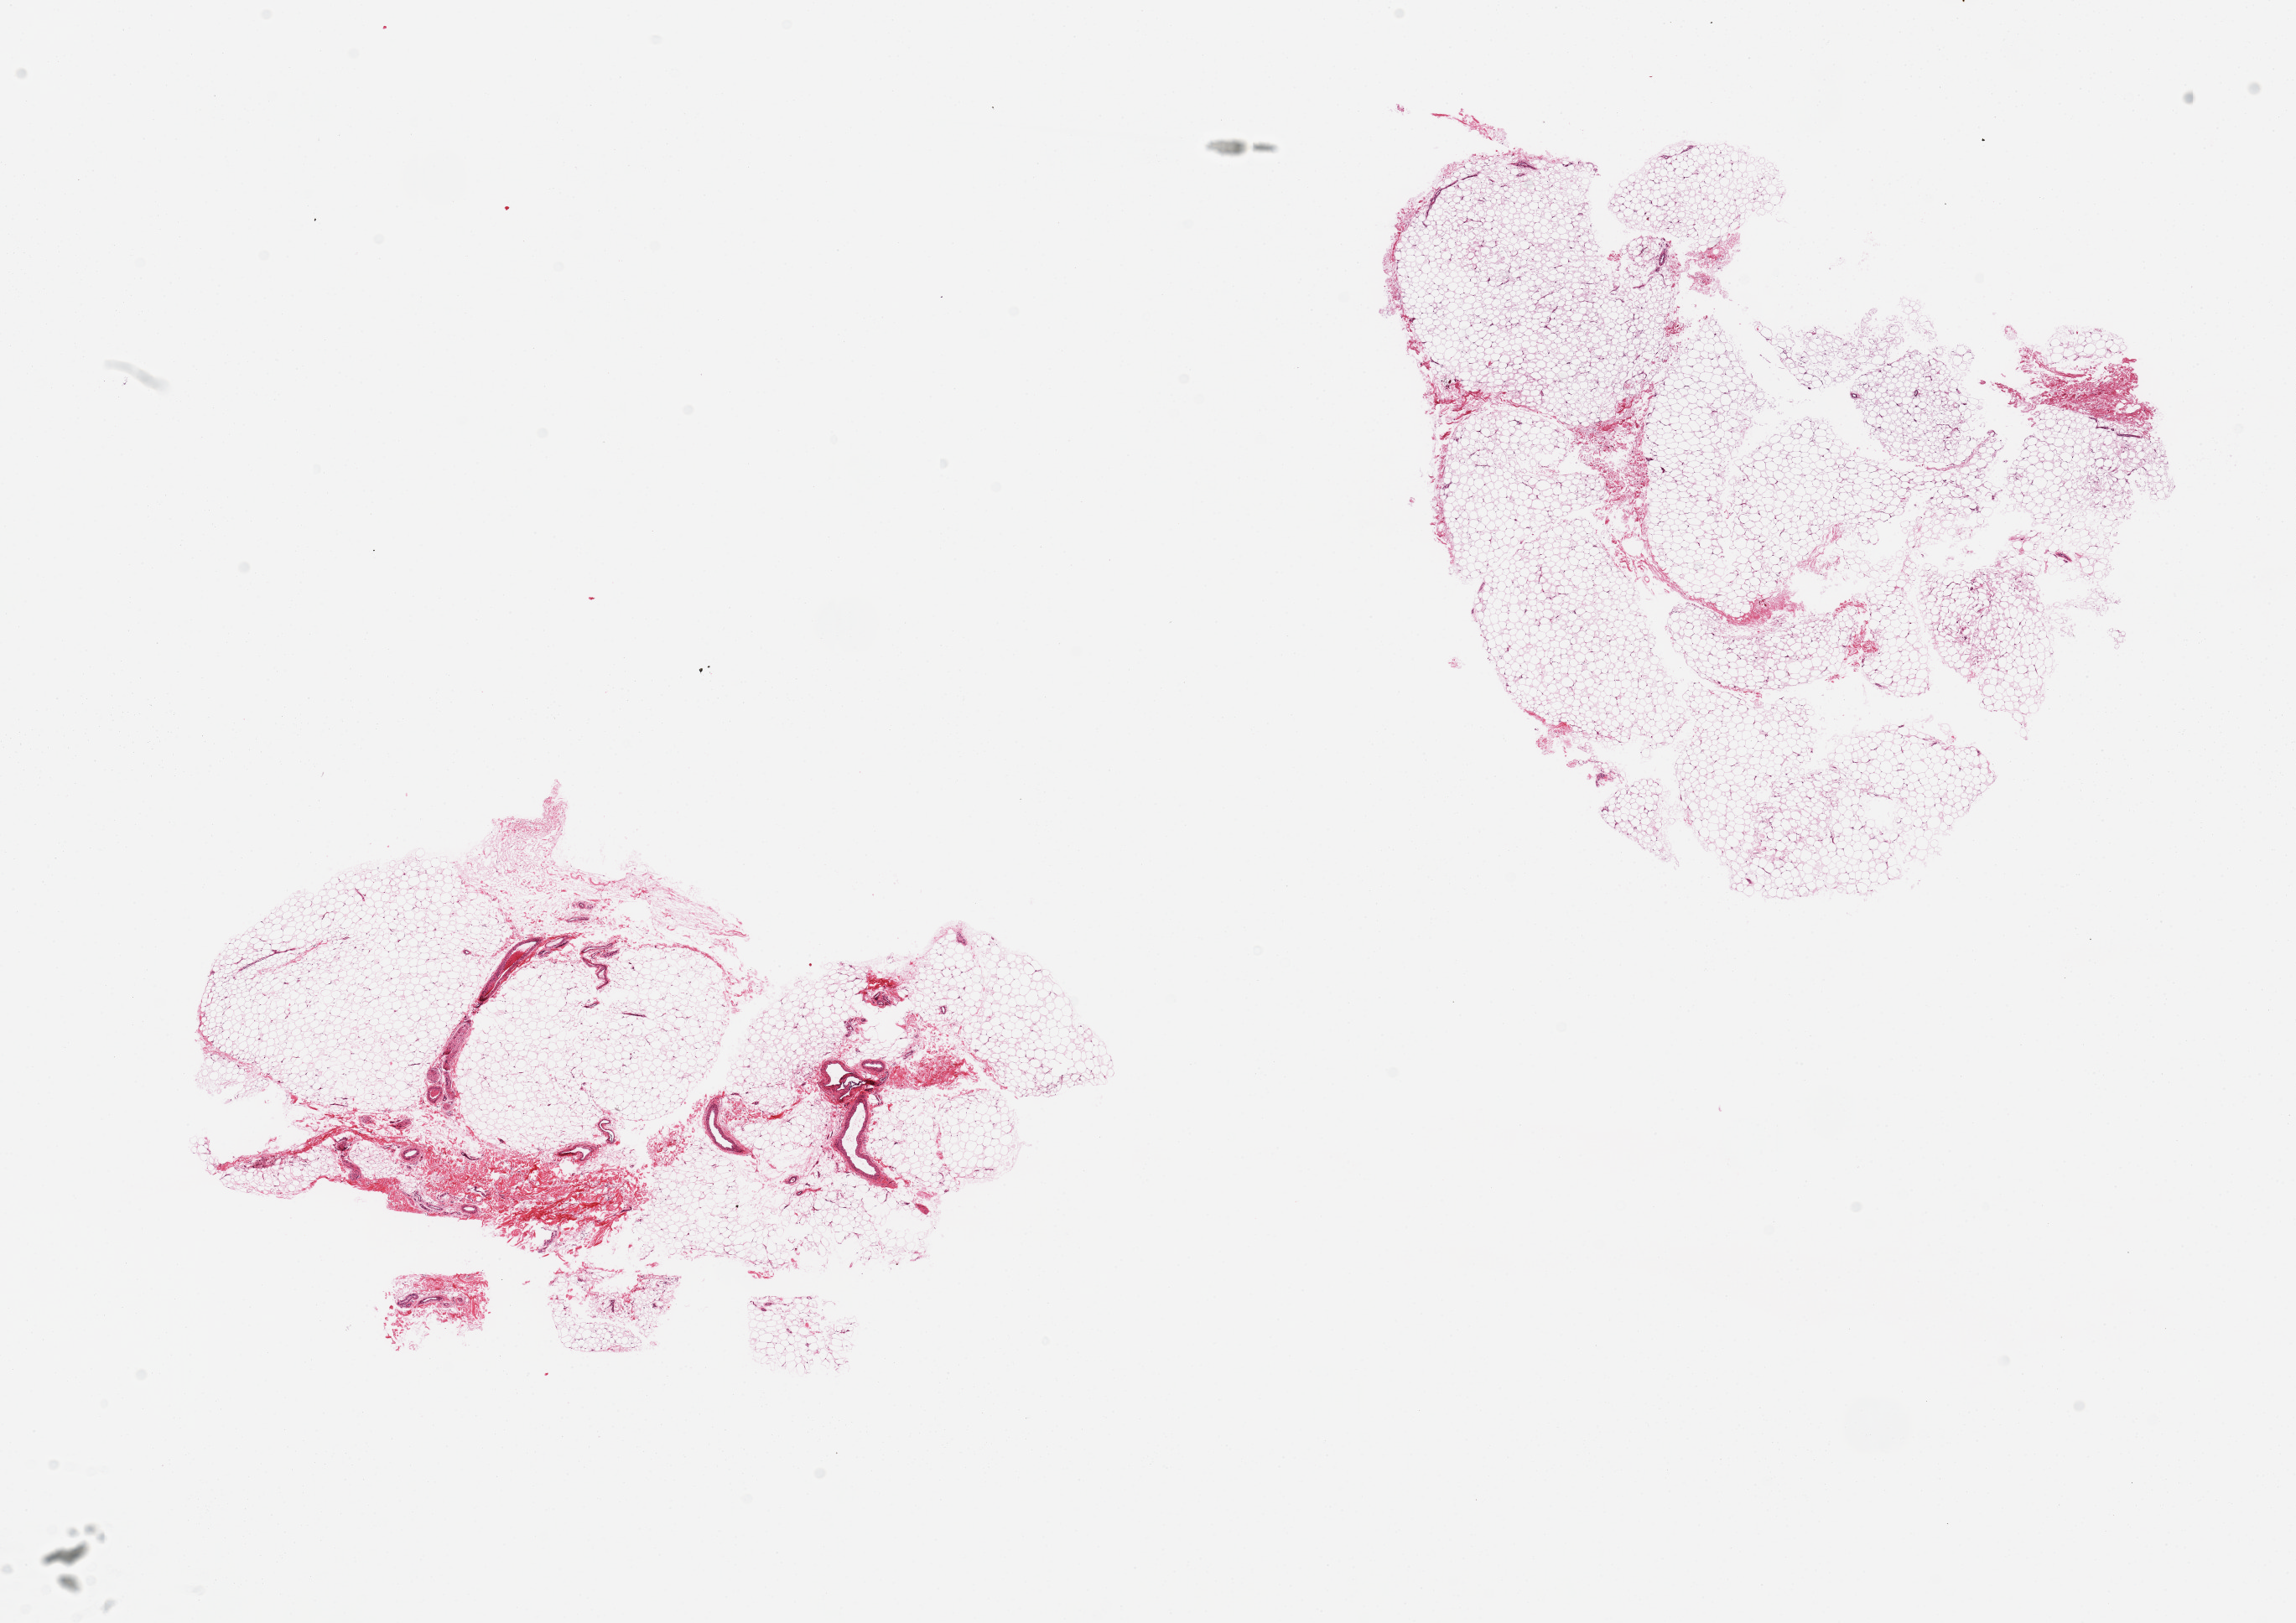
Hematoxylin and eosin (H&E) whole-slide image — a low-resolution overview of the entire scanned area, about 21.7 x 15.3 mm. PAXgene-fixed paraffin-embedded (PFPE) section. Section of adipose tissue (target tissue). Donor tissue sample. Male donor.
* pathologist's review note for this sample: 2 pieces, ~15% fibrovascular/fascial tissue